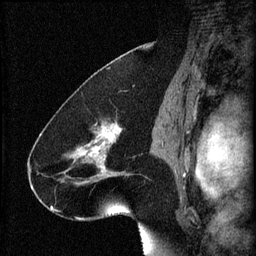
Breast MRI (dynamic contrast-enhanced), one sagittal slice. Slice 39 of 60 in the series (ordered by position). 3 images stored at this slice position (order not interpretable as contrast timing). 1.5 T. TE 4.2 ms, TR 8.2 ms. 2 mm slice thickness. 256 × 256 image matrix, field of view 180 × 180 mm. Female patient, age 41 years.
Outlined on this slice (semi-automatic segmentation, software-assisted and operator-edited):
- analysis volume of interest (the breast-tissue region the enhancement analysis was run in; not a lesion): box from (x=72, y=120) to (x=133, y=187) px
- tumour enhancement mask (voxels above the 70 % enhancement threshold inside the analysis volume of interest): (x=73, y=124)–(x=123, y=185)